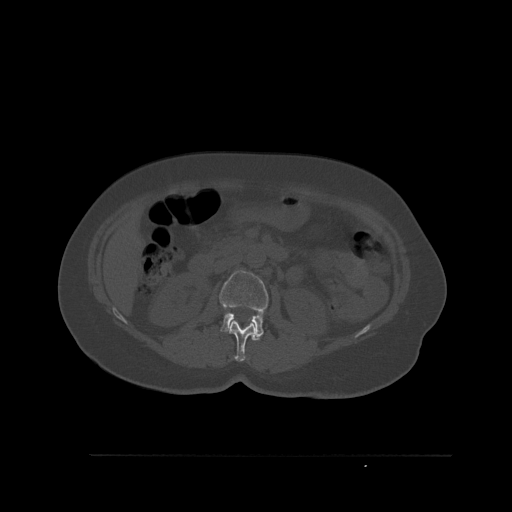
CT including the spine, one axial slice; position 254 of 527 along the scan axis; bone window (W 1800 / L 400 HU); 1.5 mm slice thickness; 512 × 512 image matrix. Patient: female, 73 years. From the clinical record (not read from this slice): primary cancer: breast; vertebrae with lytic lesions (as recorded): L2.
Structures marked on this image (semi-automatically segmented with operator editing):
- L1 vertebra: bounding box (x1, y1, x2, y2) in pixels: (228, 320, 256, 362)
- L2 vertebra: (219, 270, 268, 341)